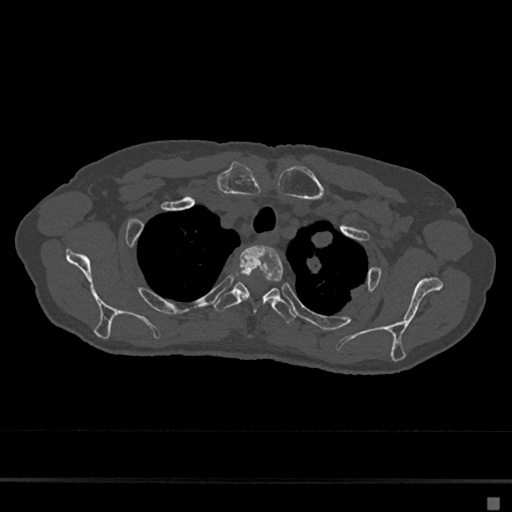
CT including the spine, one axial slice; slice 558 of 797 in the series (ordered by position); 120 kVp; bone window (W 1800 / L 400 HU); 0.5 mm slice thickness; 512 × 512 image matrix, field of view 360 × 360 mm. Female patient, age 68 years. Case-level facts recorded for this patient, not image findings: primary cancer: renal.
Outlined on this slice (semi-automatic segmentation, software-assisted and operator-edited):
- T2 vertebra: bounding box <237,245,284,296> (left, top, right, bottom; pixels)
- T3 vertebra: <212,282,296,323>